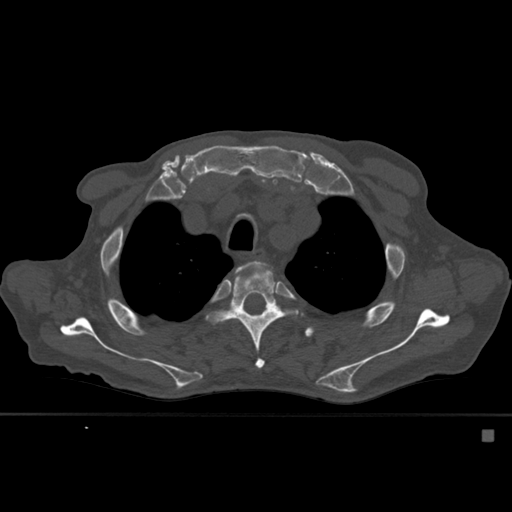
CT including the spine, one axial slice. Bone window (W 1800 / L 400 HU). 1.5 mm slice thickness. 512 × 512 image matrix. Patient: male, 78 years. Case-level facts recorded for this patient, not image findings: primary cancer: prostate.
Structures marked on this image (semi-automatically segmented with operator editing):
- T3 vertebra: bounding box [x1, y1, x2, y2] px = [235, 261, 259, 279]
- T4 vertebra: [212, 261, 297, 369]